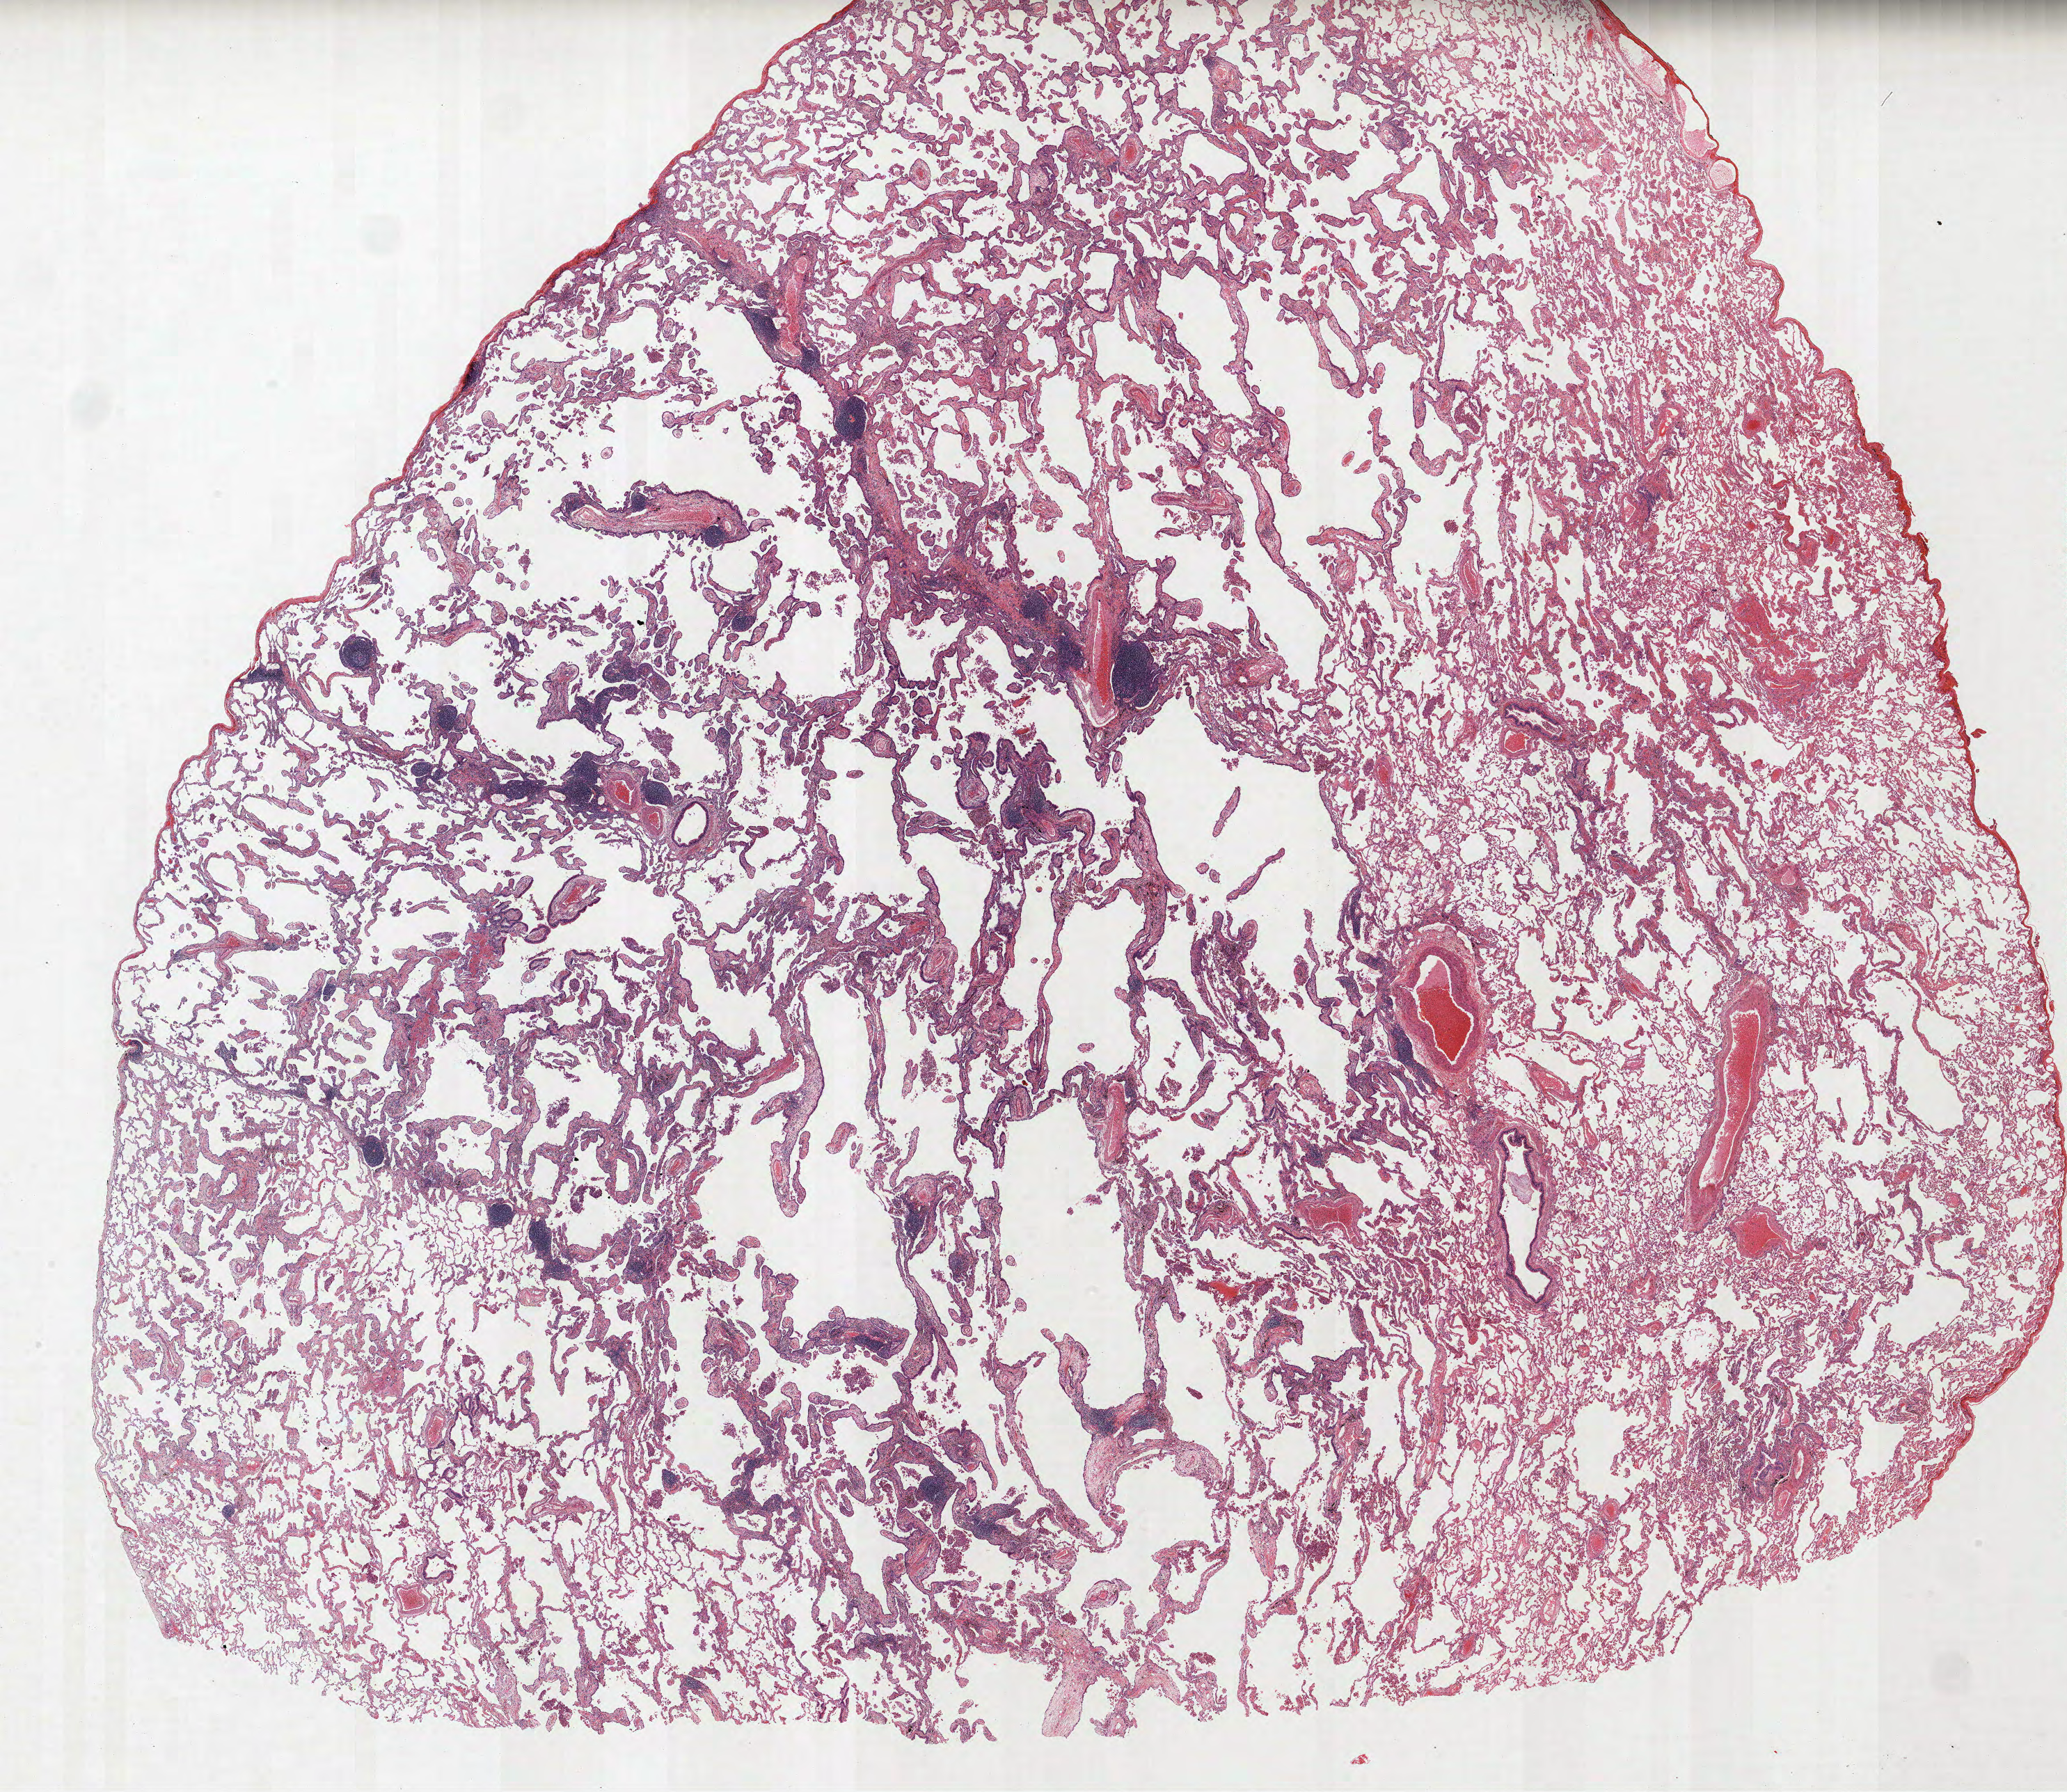
Whole-slide histology image, H&E — low-resolution overview of the scanned area, about 23.8 x 20.6 mm (acquisition: 40x scan), formalin-fixed paraffin-embedded (FFPE) section, lung. Female patient, aged 56 at enrolment. Current smoker at enrolment.
Participant's lung-cancer diagnosis: Adenocarcinoma, NOS.